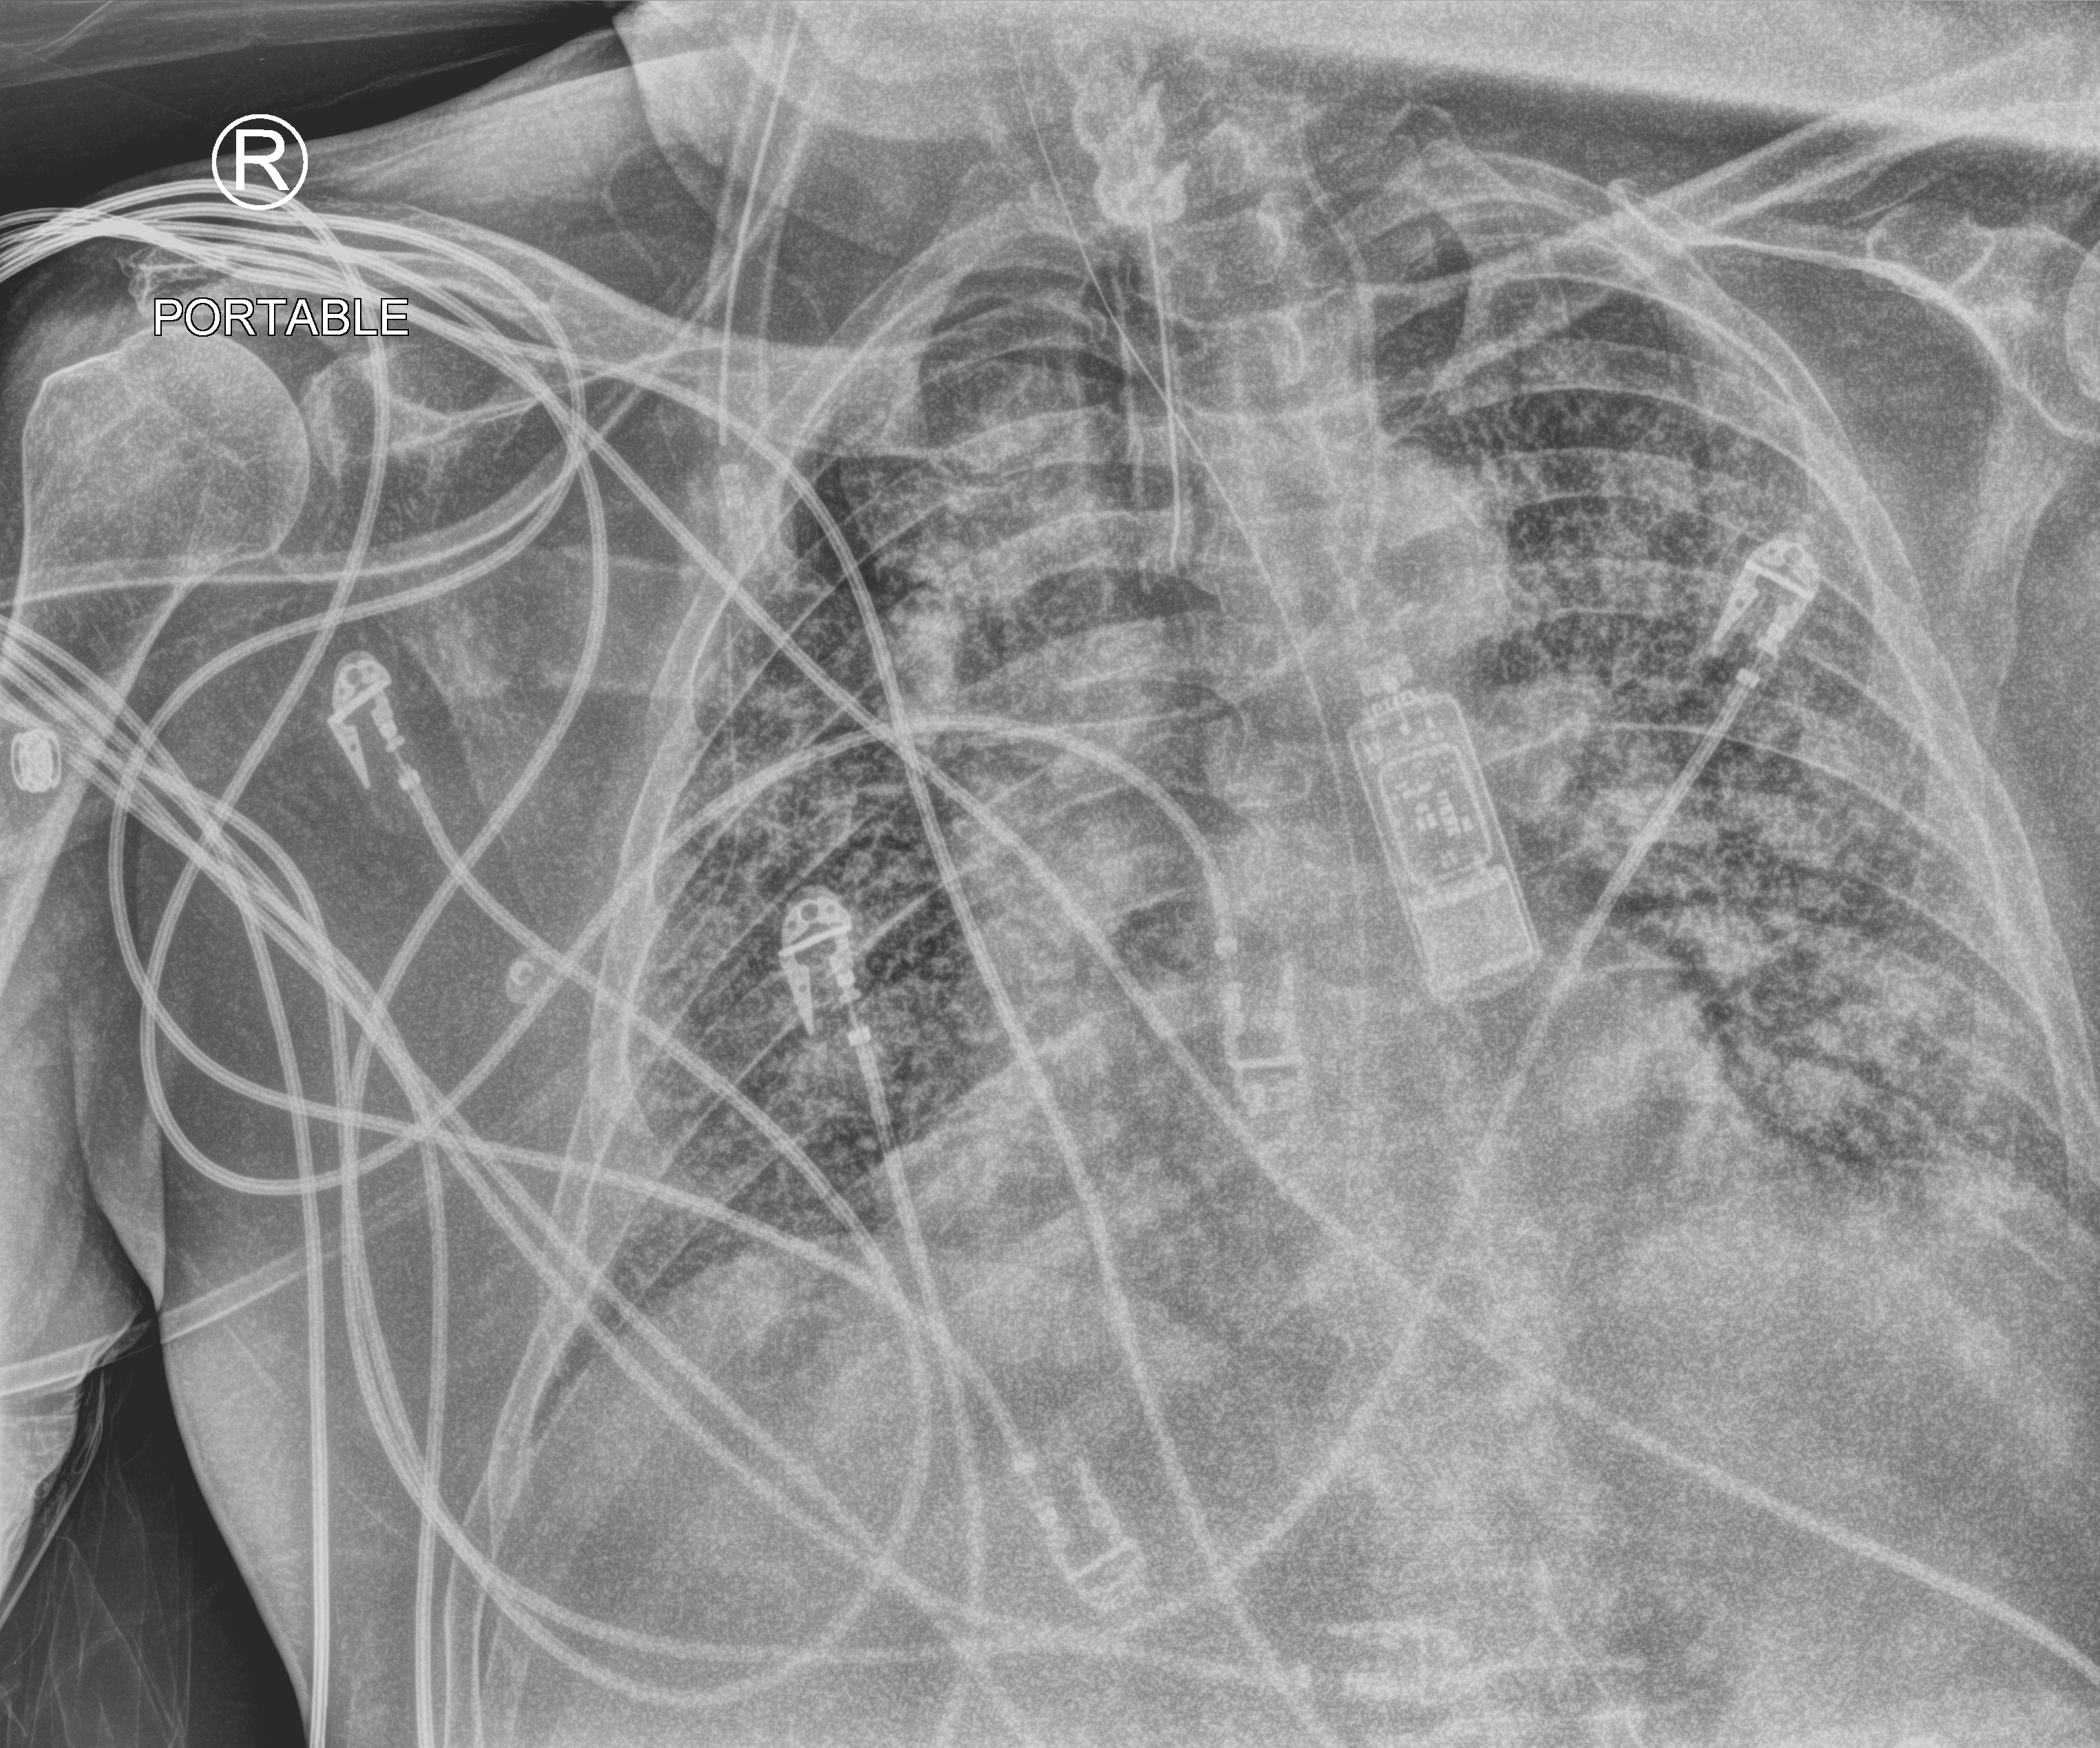
Bedside chest radiograph (computed radiography). Male patient hospitalised with COVID-19, age 60–74 years.
From the hospital-stay record, not from the radiograph (when in the stay this image was taken is not recorded):
- other chronic lung disease (admission record): yes
- mechanically ventilated during this hospital stay: yes
- admitted to intensive care during this hospital stay: yes